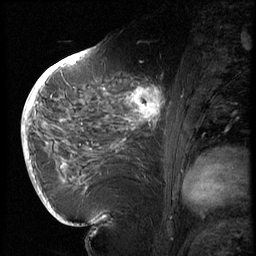
Breast MRI (dynamic contrast-enhanced), one sagittal slice; slice 32 of 72 in the series (ordered by position); 3 images stored at this slice position (order not interpretable as contrast timing); 1.5 T; TE 4.2 ms, TR 8.9 ms; 2.5 mm slice thickness; 256 × 256 image matrix, field of view 200 × 200 mm. Patient: female, 56 years. From the clinical record (not read from this slice): setting: breast cancer imaged before/during neoadjuvant chemotherapy.
Outlined on this slice (semi-automatic segmentation, software-assisted and operator-edited):
- analysis volume of interest (the breast-tissue region the enhancement analysis was run in; not a lesion): bounding box (x1, y1, x2, y2) in pixels: (114, 76, 177, 138)
- tumour enhancement mask (voxels above the 140 % enhancement threshold inside the analysis volume of interest): (126, 86, 165, 126)